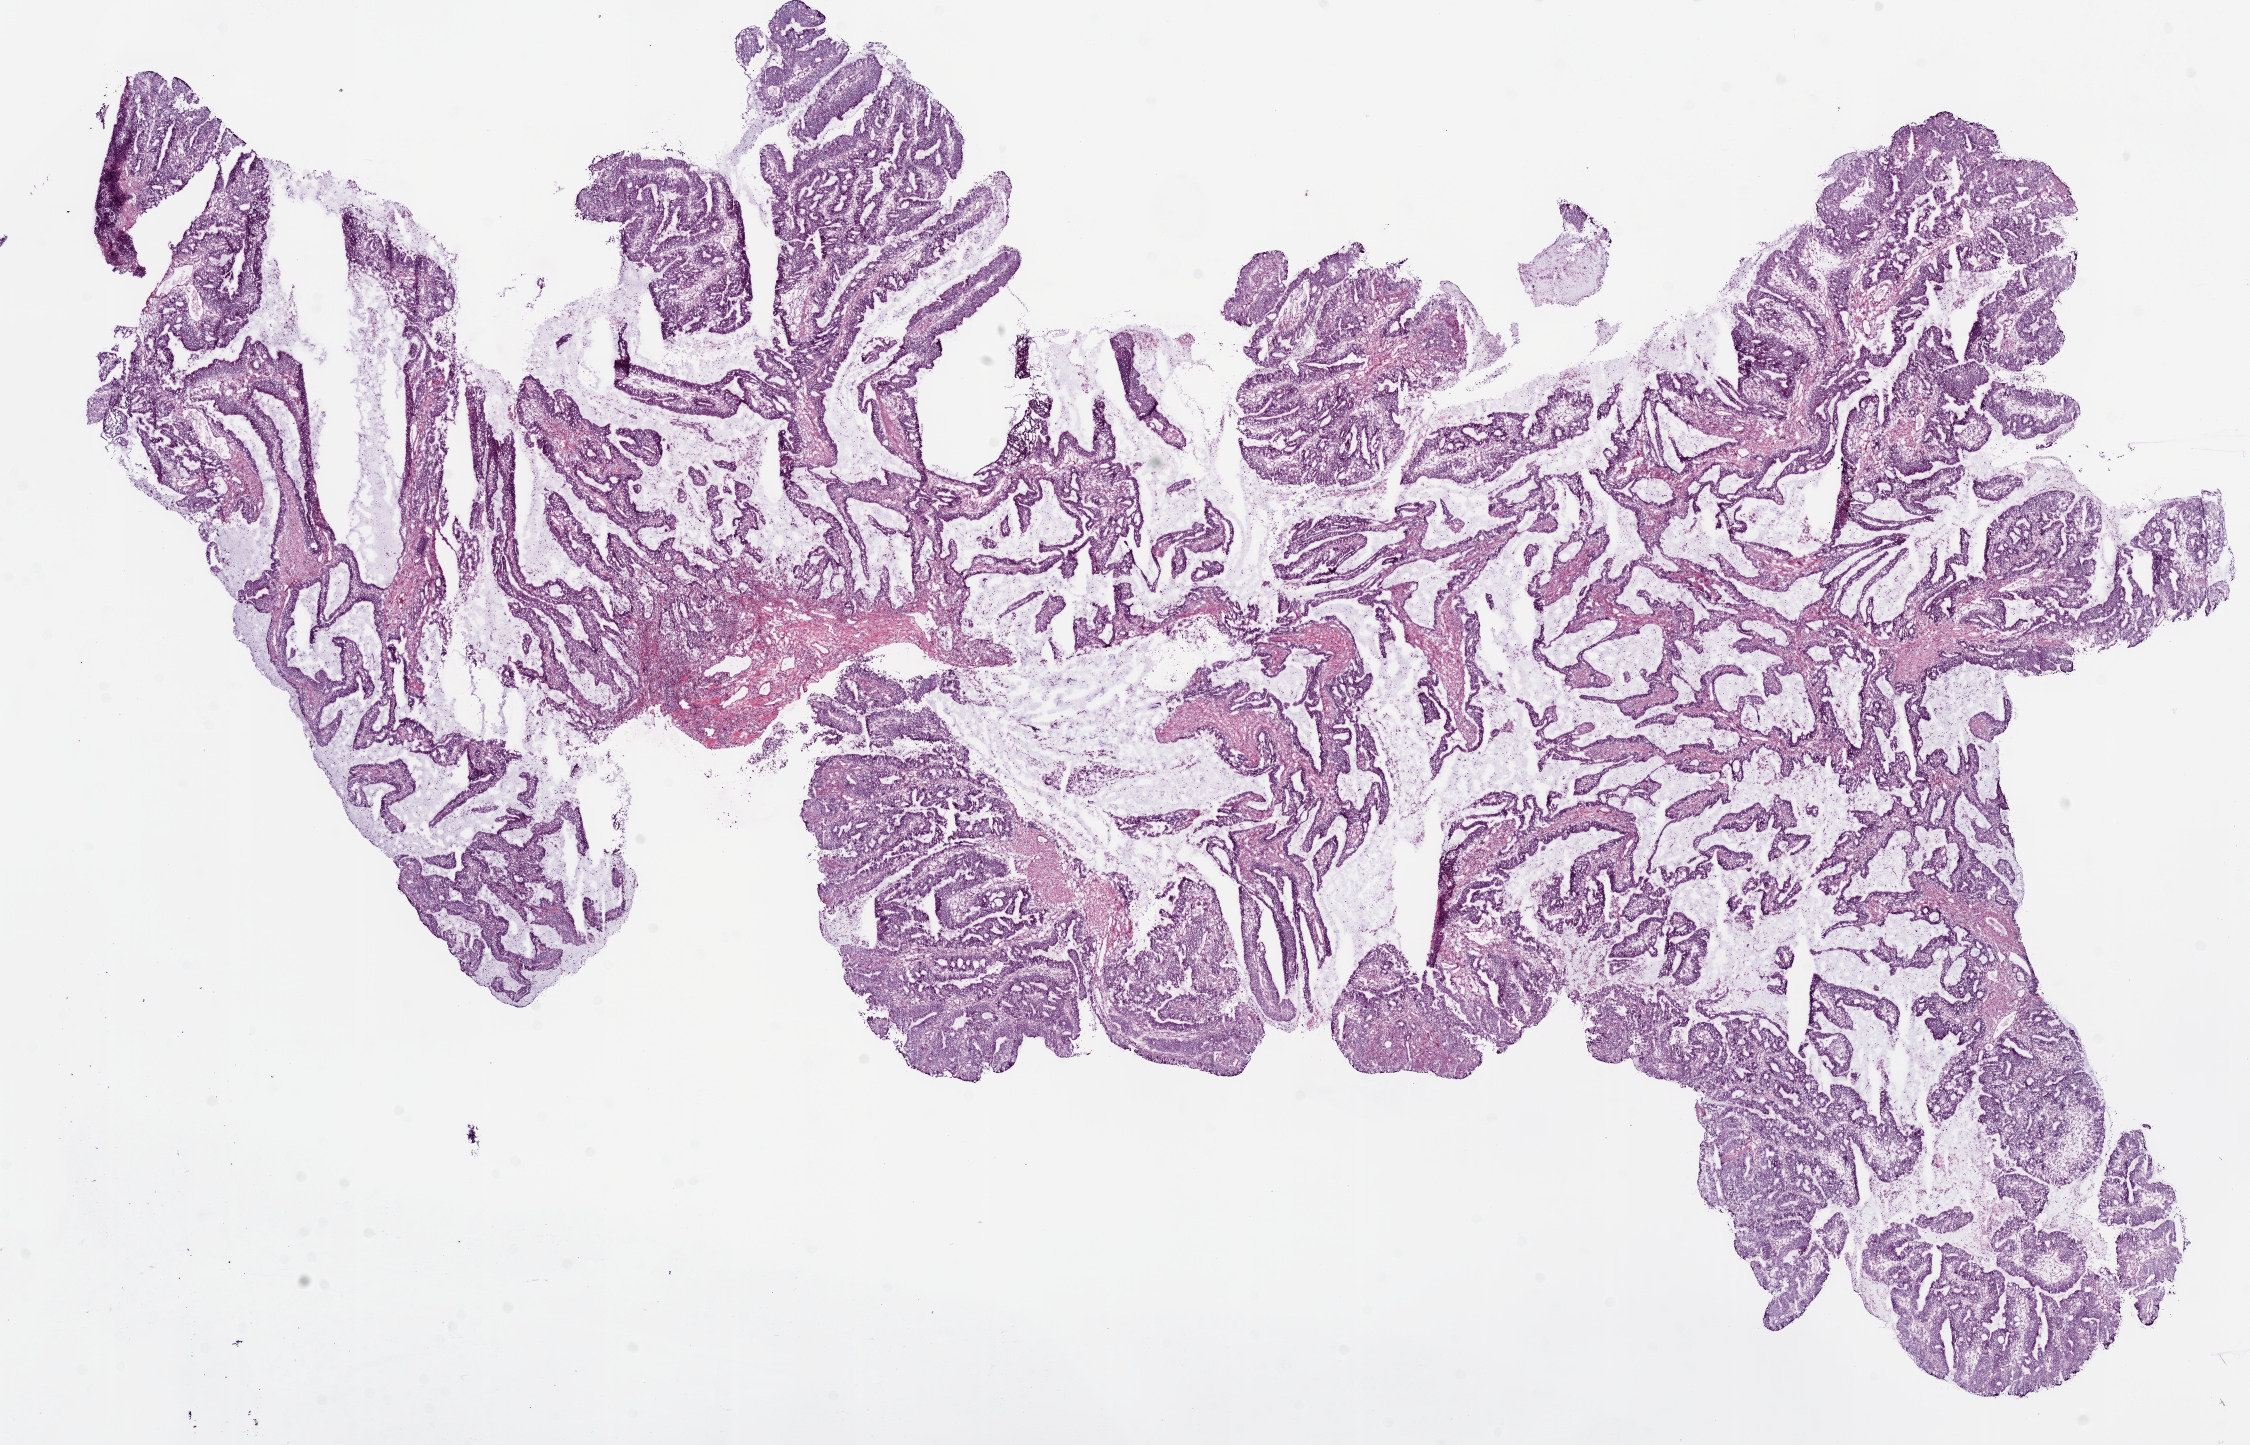
Whole-slide histology image, H&E-stained — low-resolution overview of the scanned area, about 18.1 x 11.6 mm. Frozen section from the bottom of the tissue portion. Sample: primary tumour, colon. Male patient; age at initial diagnosis 61 years. Pathologist review of this section (percent, as recorded): tumour cells 75%, tumour nuclei 80%, normal cells 10%, stromal cells 15%, necrosis 0%.
AJCC pathologic stage: I. Pathologic diagnosis: Adenocarcinoma, NOS (sigmoid colon). Lymph nodes positive (case pathology): 0 of 17 examined.